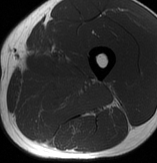
MRI of an extremity soft-tissue mass, one axial slice; position 36 of 70 along the scan axis; MR volume resampled by the dataset authors to the PET/CT grid (not the native acquisition matrix); 3.27 mm slice thickness; 157 × 163 image matrix, field of view 153 × 159 mm. Male patient. Case-level facts recorded for this patient, not image findings: histological type: extraskeletal osteosarcoma; grade: high; site of the primary tumour: left adductur.
Annotated regions visible in this slice (expert contour drawn on MRI and transferred to this co-registered scan by the dataset authors):
- gross tumour volume (mass): bounding box (x1, y1, x2, y2) in pixels: (19, 67, 118, 121)